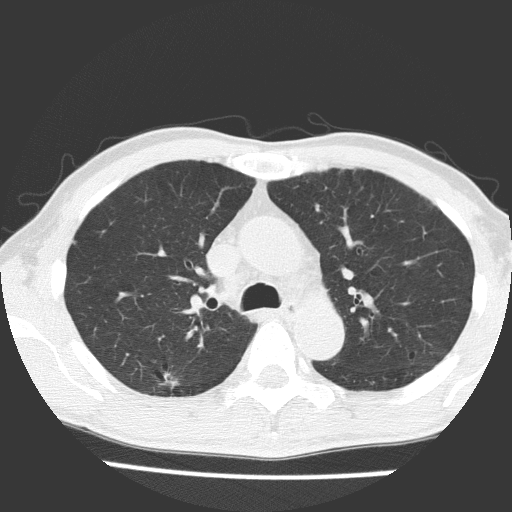
Chest CT (low-dose screening protocol), one axial image; baseline annual screen; lung window (W 1500 / L -600 HU). Male participant, aged 66 years at enrolment. Current smoker at enrolment.
• Expert-annotated lung lesion, bounding box (x1, y1, x2, y2) in pixels: (133, 354, 196, 410).
• The exam's reader record, not a measurement of the box and not confirmed to be the same lesion: non-calcified nodule or mass ≥4 mm, right upper lobe, 15 × 10 mm, spiculated (stellate) margins, soft tissue attenuation.
• Participant outcome: lung cancer diagnosed 43 days after this screen — adenocarcinoma, NOS, right upper lobe, moderately differentiated (G2), stage IB (AJCC 6th edition), 11 mm at pathology.